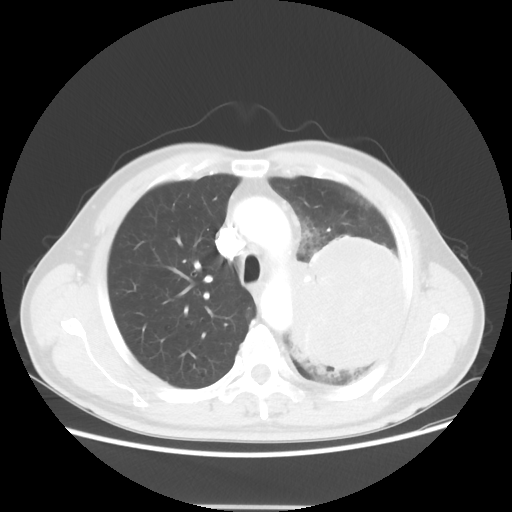
Chest CT, one axial slice; reconstruction kernel STANDARD; 100 kVp; lung window (W 1500 / L -600 HU); 5 mm slice thickness; 512 × 512 image matrix. Patient: male, 60 years. Case-level facts recorded for this patient, not image findings: clinical TNM (as recorded): T4 N1 M1a; histopathological grade: G3.
Annotated regions visible in this slice (rectangle marked by the reading radiologist):
- lung tumour (recorded histology: large cell carcinoma): bounding box <289,242,408,393> (left, top, right, bottom; pixels)